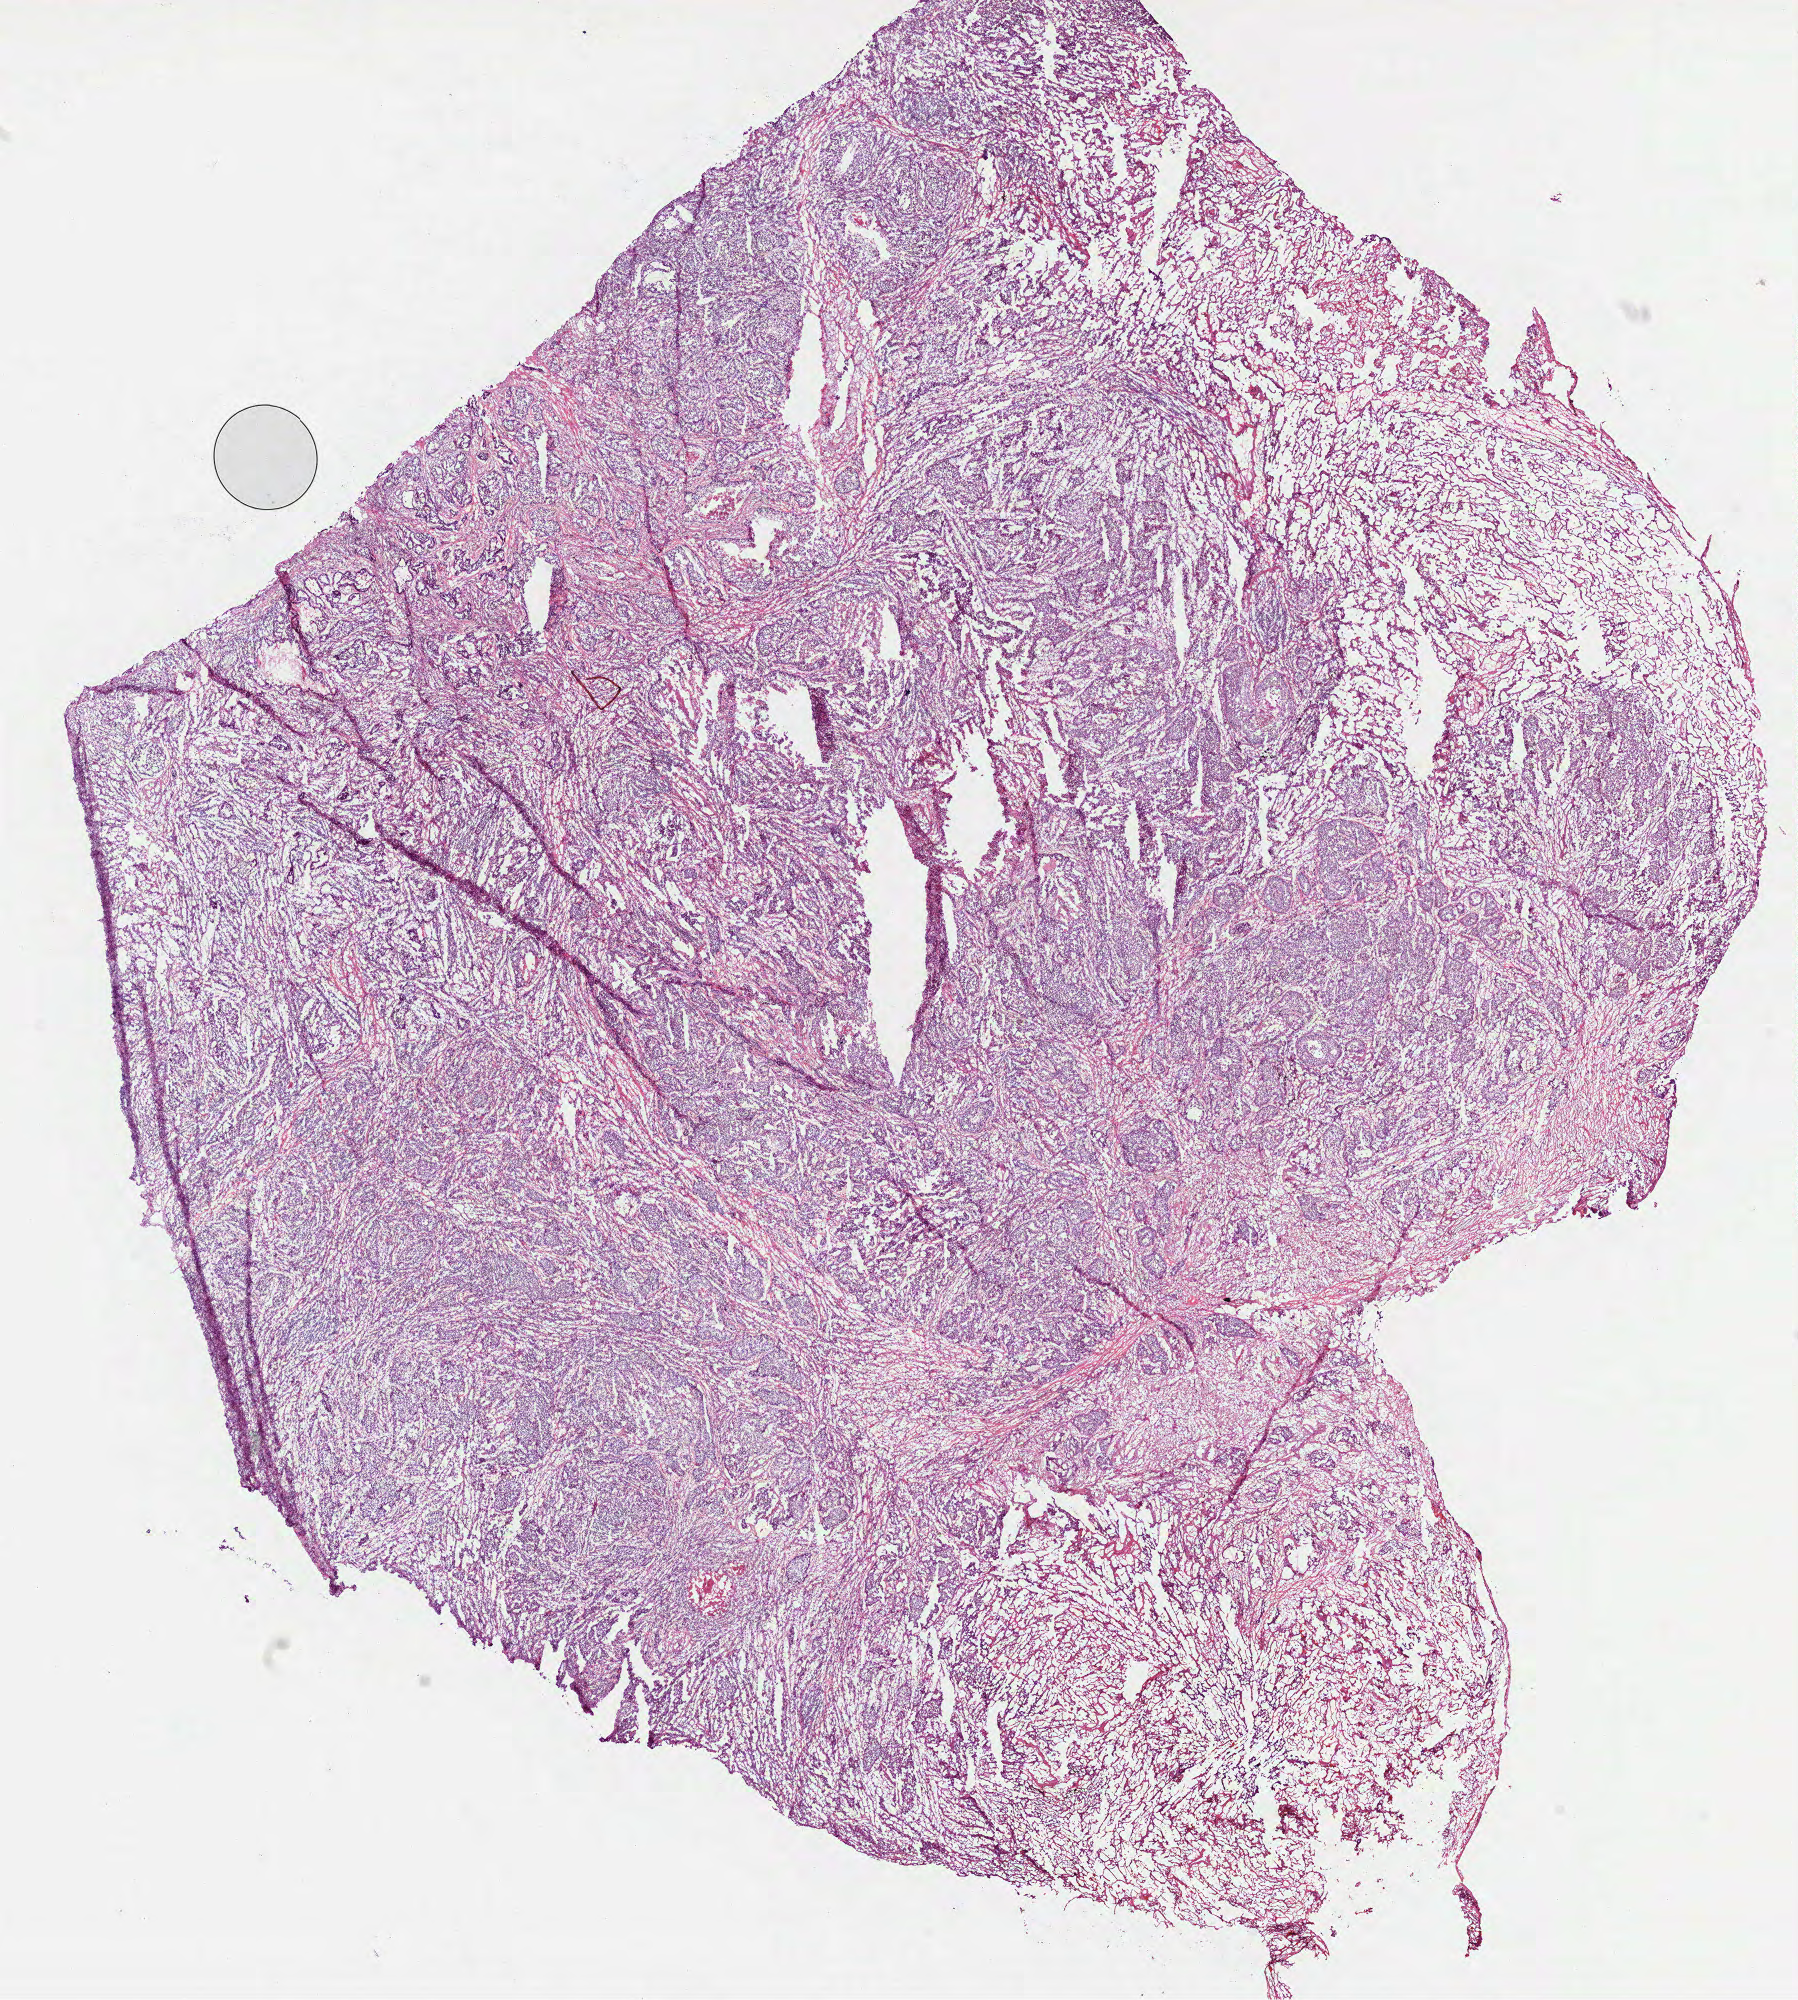
H&E whole-slide image, low-resolution overview of the scanned area, about 14.5 x 16.1 mm; frozen section from the top of the tissue portion; primary tumour sample from the lung. Patient: male, age at initial diagnosis 66 years. Composition of this section per pathologist review: tumour cells 60%, tumour nuclei 65%, normal cells 15%, stromal cells 15%, necrosis 10%. Inflammatory infiltration, as recorded: lymphocyte infiltration 10%.
Pathologic diagnosis: Adenocarcinoma, NOS (upper lobe, lung). AJCC pathologic stage: IV (7th edition). TNM: T2 N0 M1.